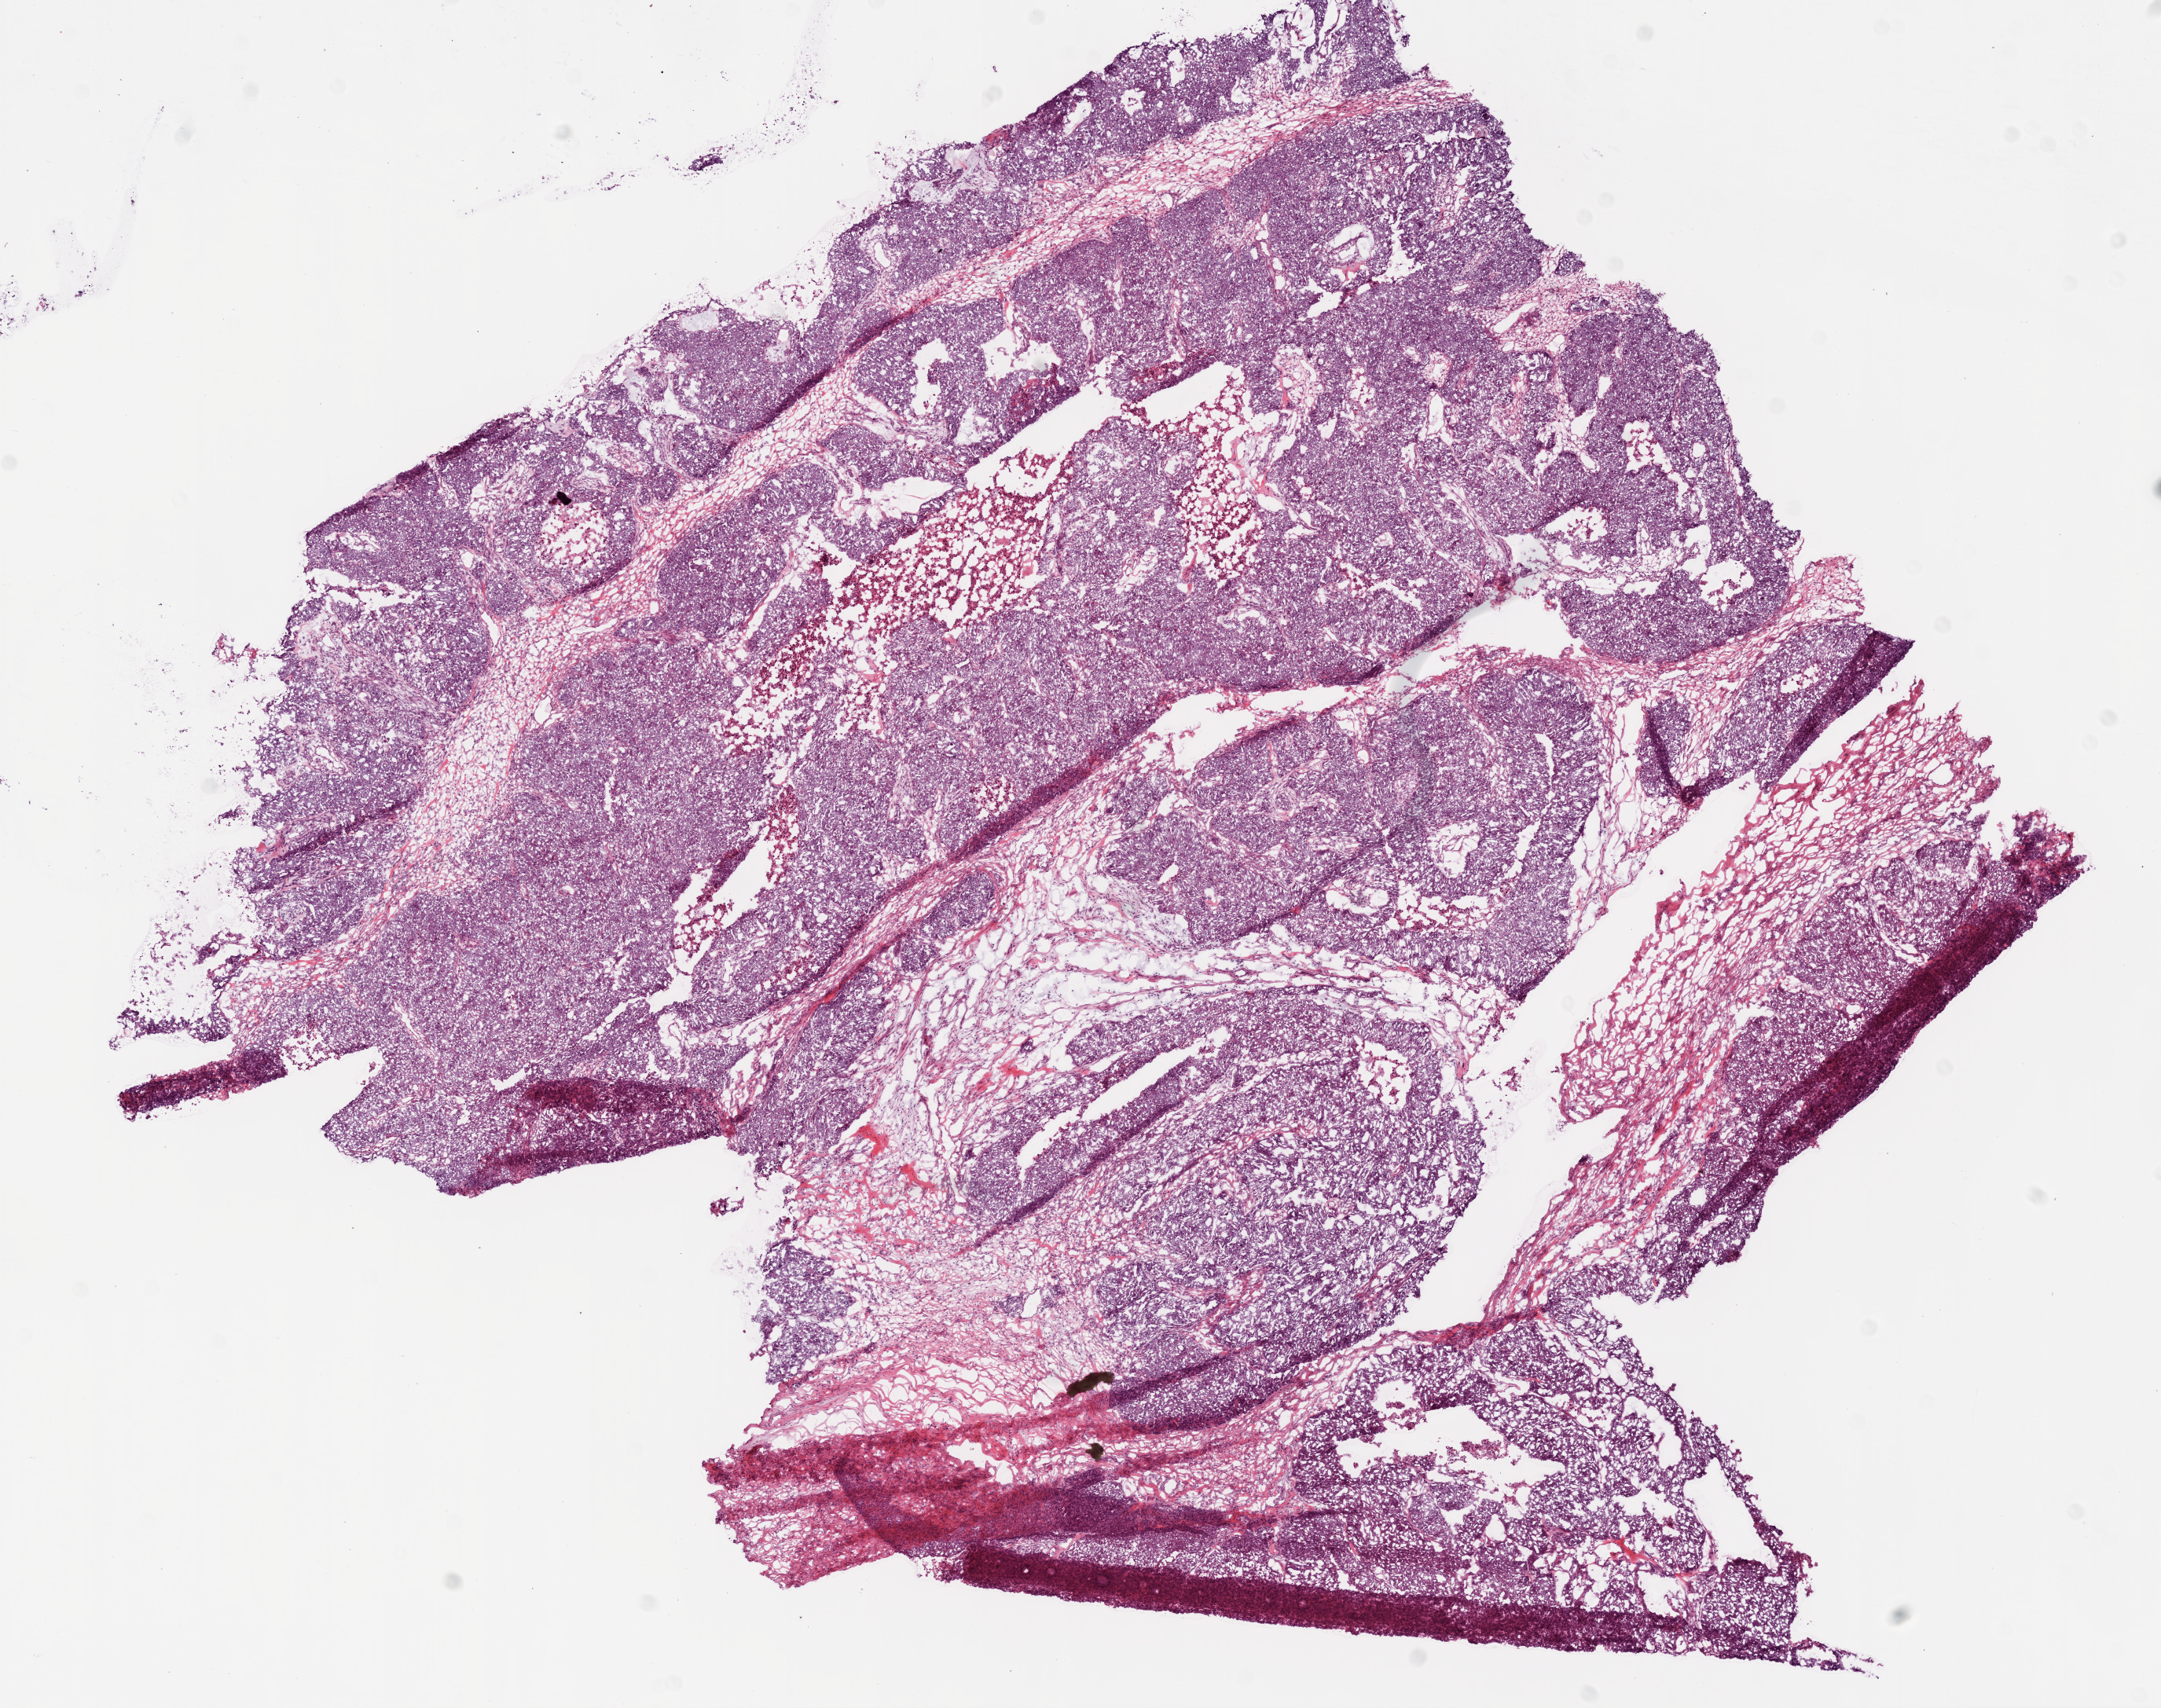
Whole-slide histology image, H&E-stained, shown as a low-resolution overview of the whole scanned area (about 11.0 x 8.7 mm), frozen section from the bottom of the tissue portion, primary tumour sample from the ovary. Female patient; age at initial diagnosis 58 years. Histologic grade: G3 (poorly differentiated). Pathologist review of this section (percent, as recorded): tumour cells 80%, tumour nuclei 95%, normal cells 0%, stromal cells 15%, necrosis 5%.
Histologic diagnosis: Serous cystadenocarcinoma, NOS. FIGO stage: IIIB.